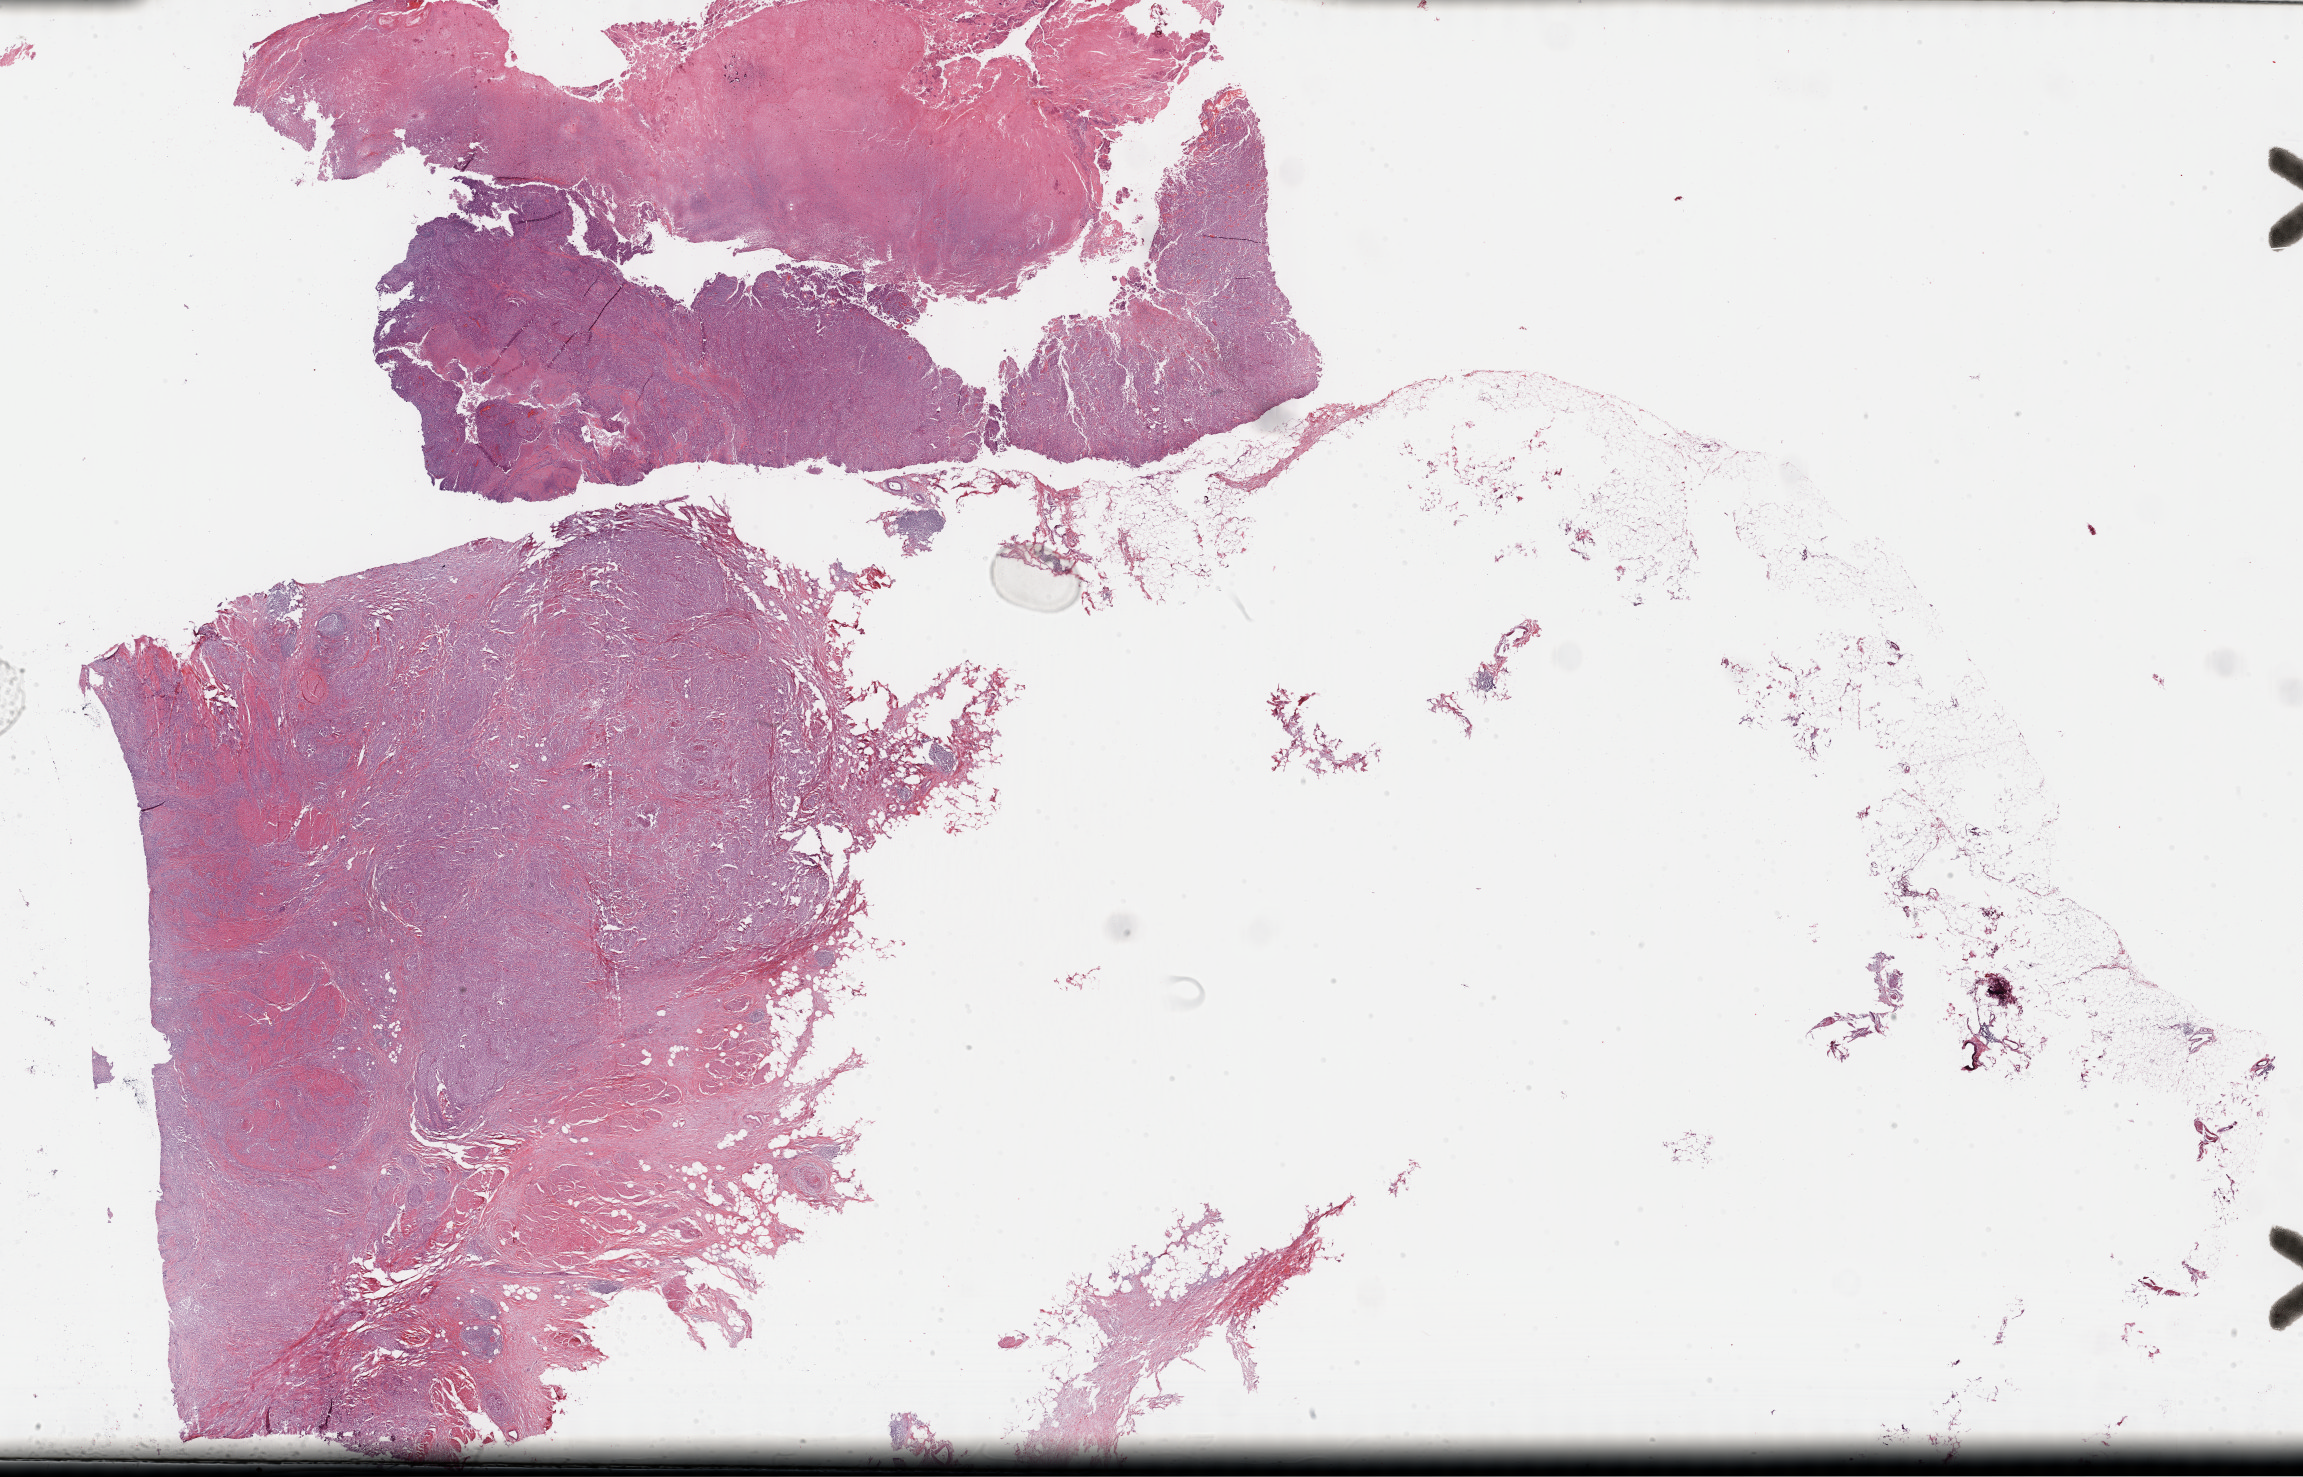
Digitized H&E tissue section (whole slide) — whole scanned area (about 37.2 x 23.9 mm) shown as a low-resolution overview; formalin-fixed paraffin-embedded (FFPE) diagnostic section; bladder, primary tumour sample. Patient: male, age at initial diagnosis 76 years. Histologic grade: high grade.
Lymph nodes positive (case pathology): 0 of 104 examined. AJCC pathologic stage: III (6th edition). TNM: T3b N0 MX. Pathologic diagnosis: Transitional cell carcinoma.